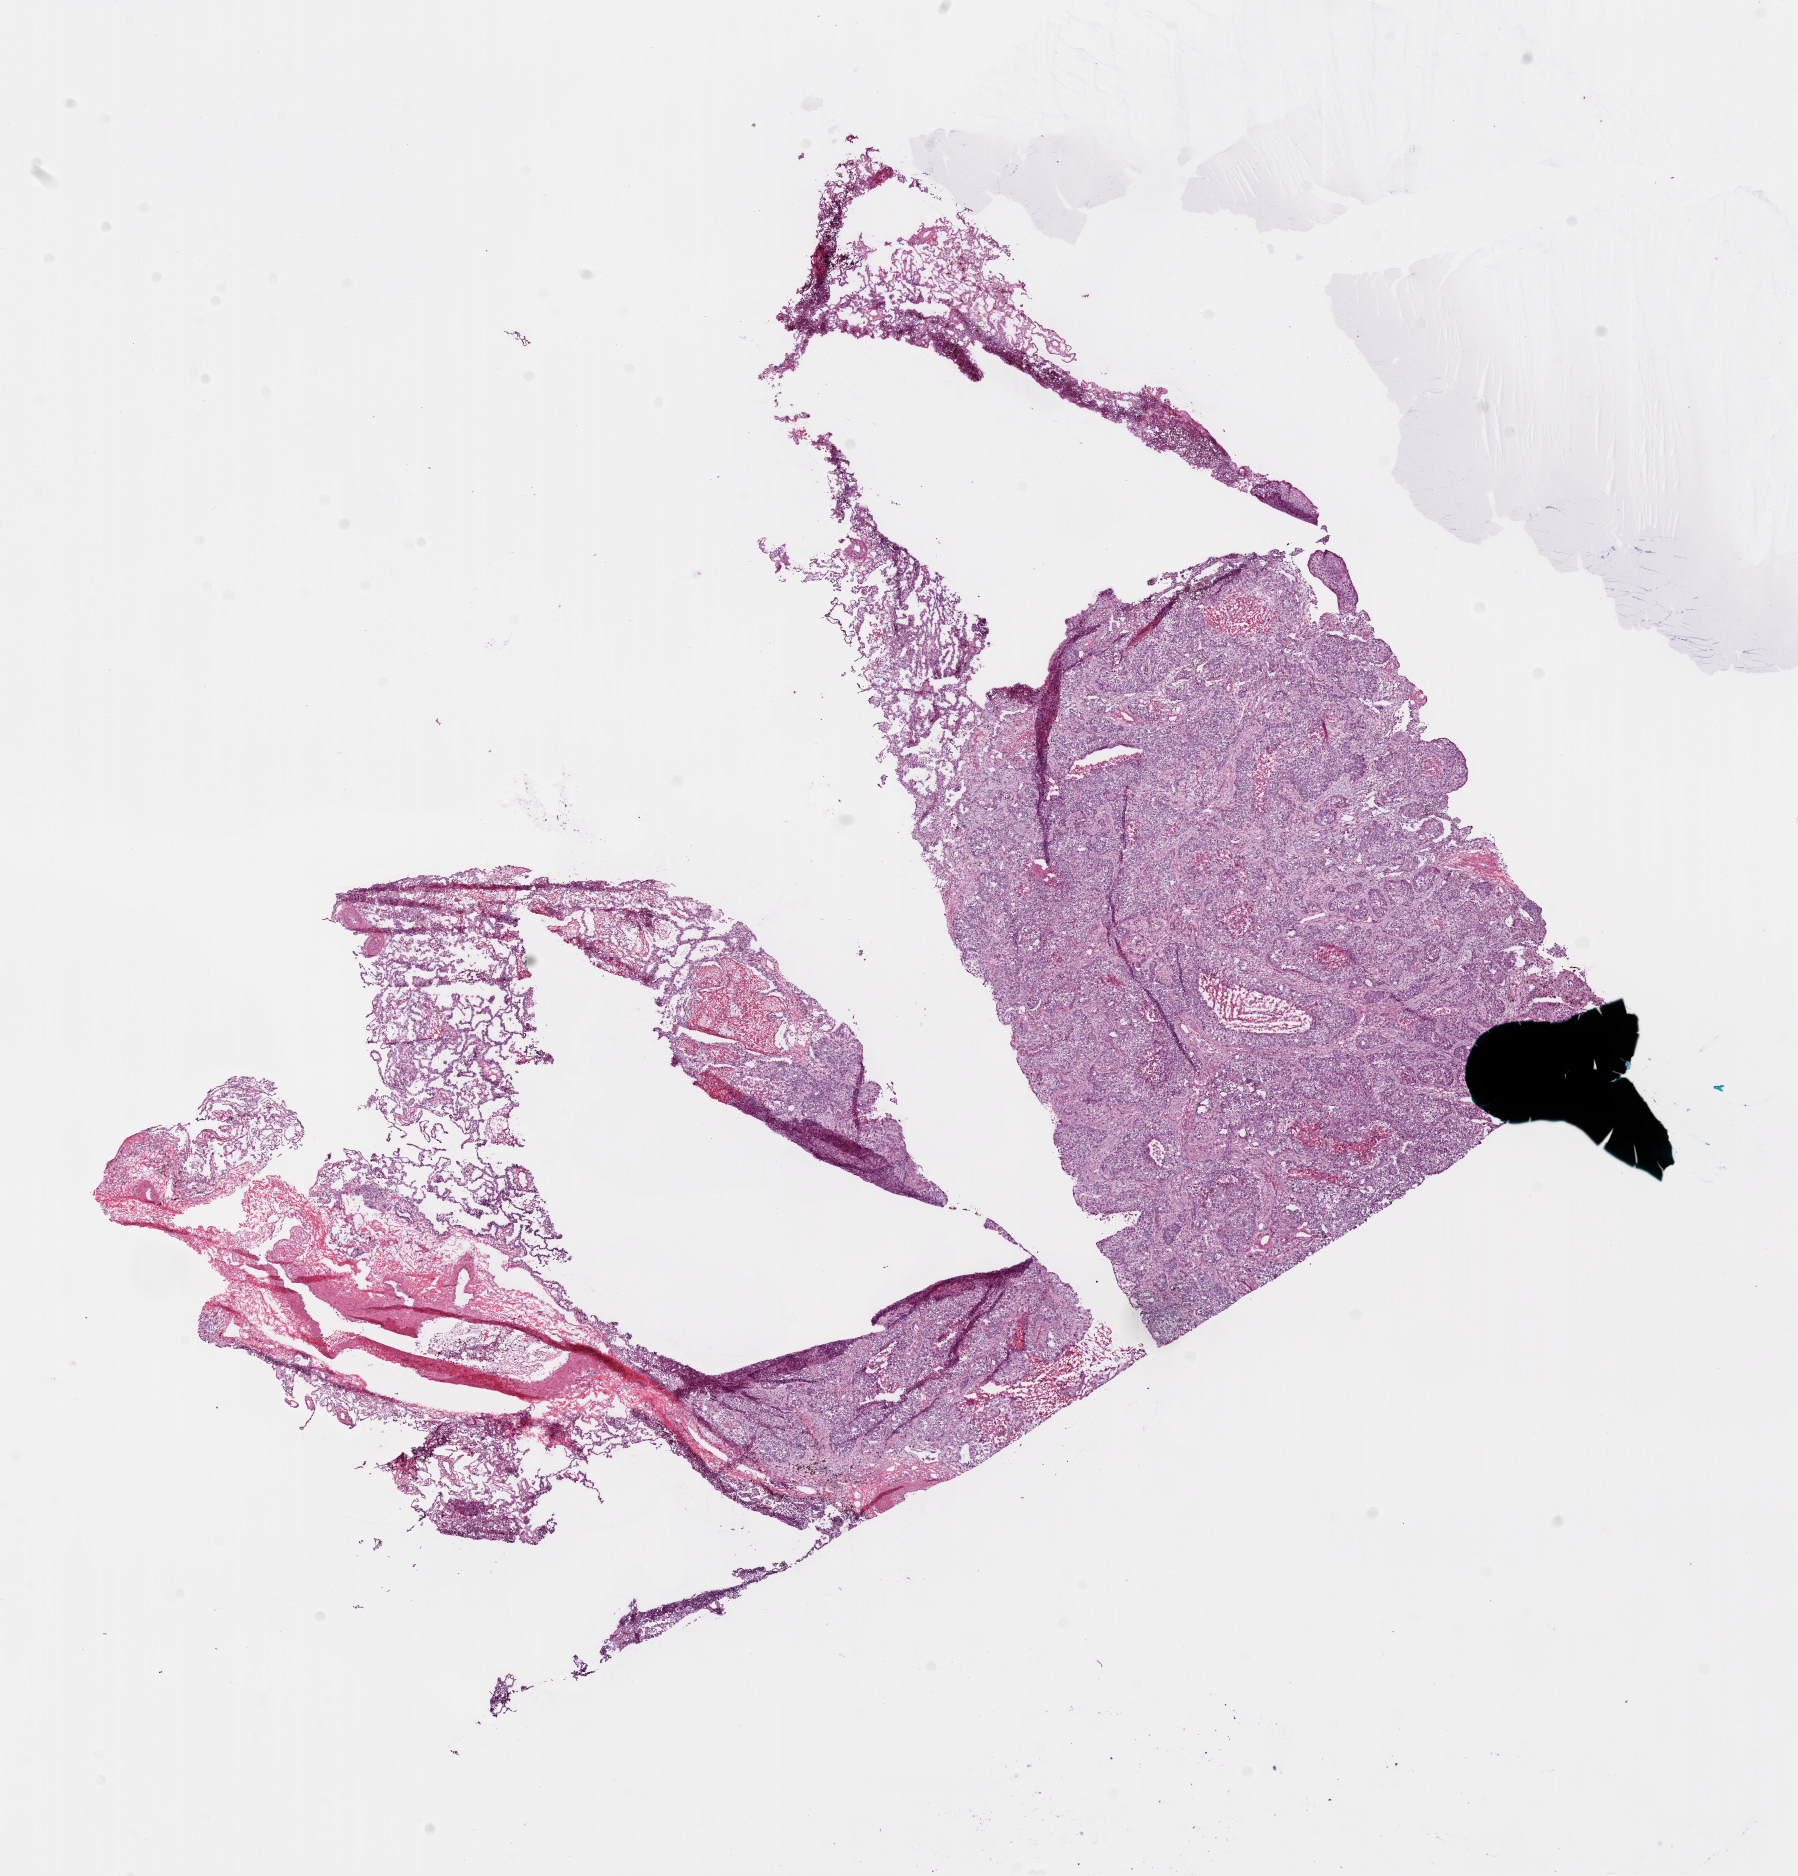
Digitized H&E tissue section (whole slide) — low-resolution overview of the scanned area, about 14.5 x 15.1 mm (from a 20x scan). Frozen section from the bottom of the tissue portion. Lung, primary tumour sample. Male, age 65 years at initial diagnosis. Composition of this section per pathologist review: tumour nuclei 70%, necrosis 3%.
Histologic diagnosis: Squamous cell carcinoma, NOS. AJCC pathologic stage: IB.